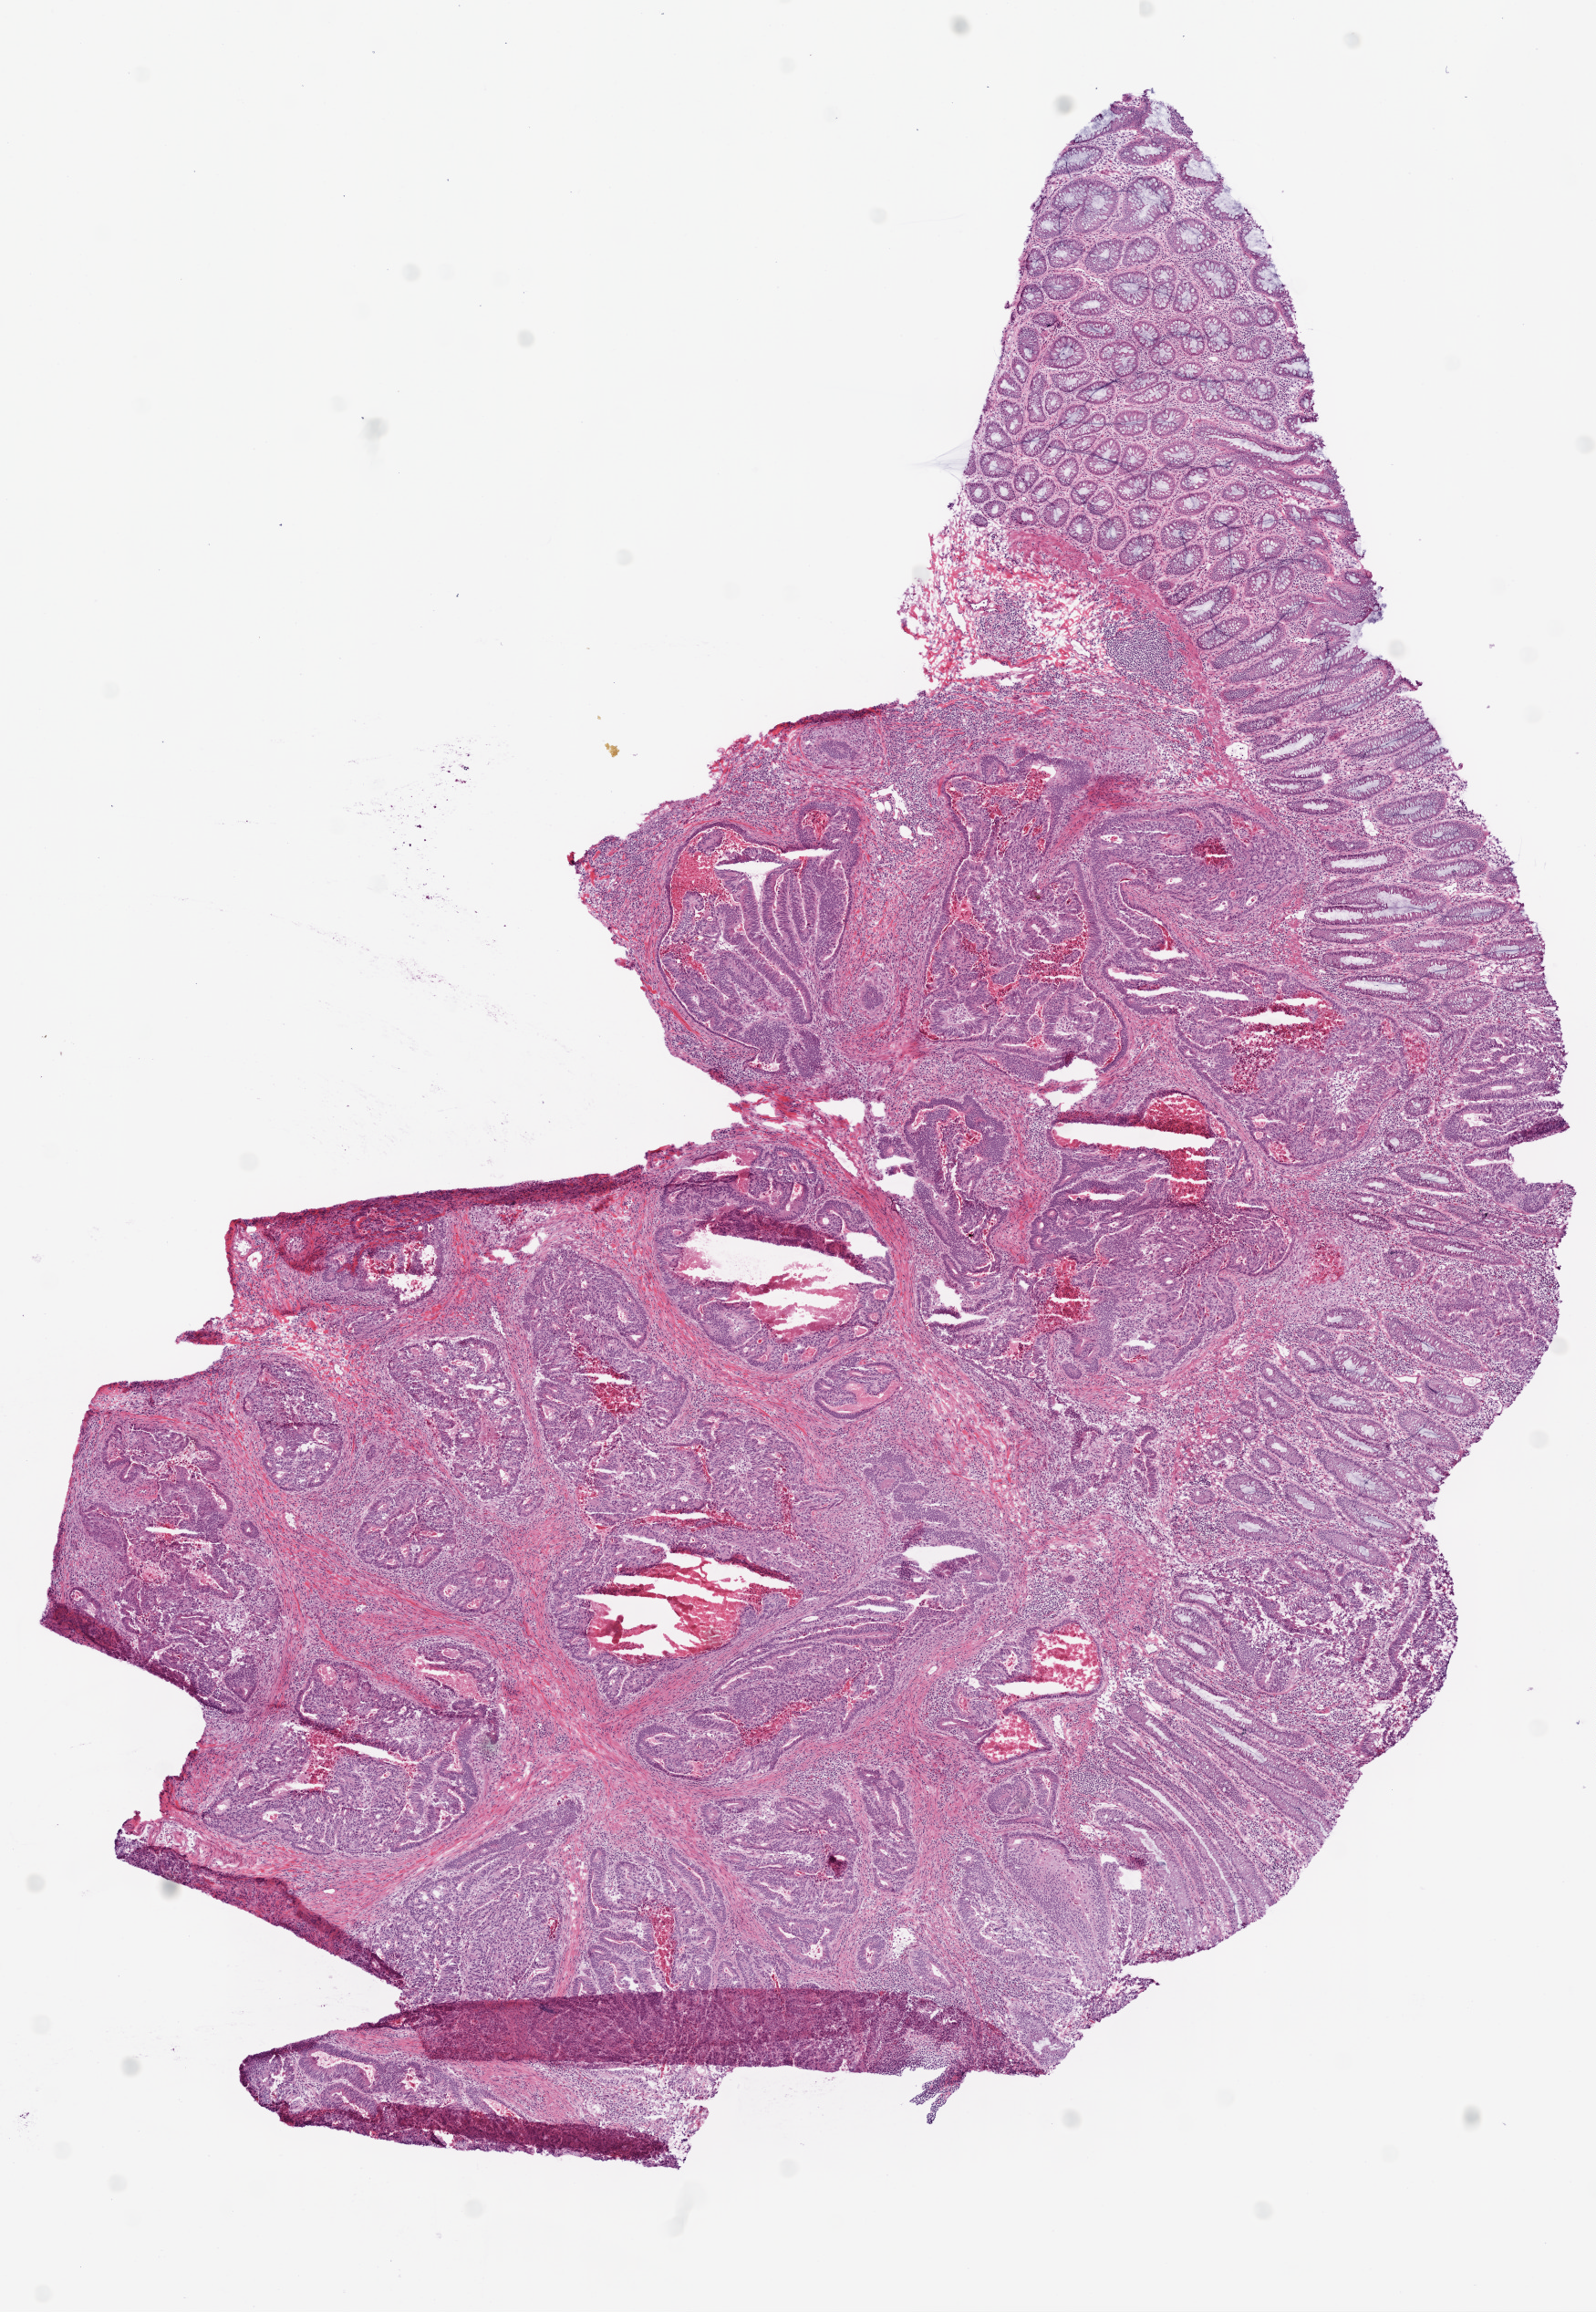
H&E-stained whole-slide image, whole scanned area (about 7.0 x 10.2 mm, from a 20x scan) shown as a low-resolution overview; frozen section from the top of the tissue portion; primary tumour sample from the colon. Male, age 59 years at initial diagnosis. Composition of this section per pathologist review: tumour cells 55%, tumour nuclei 70%, normal cells 15%, stromal cells 15%, necrosis 15%.
- lymph nodes positive (case pathology): 0 of 13 examined
- AJCC pathologic stage: IIA (6th edition)
- diagnosis: Adenocarcinoma, NOS